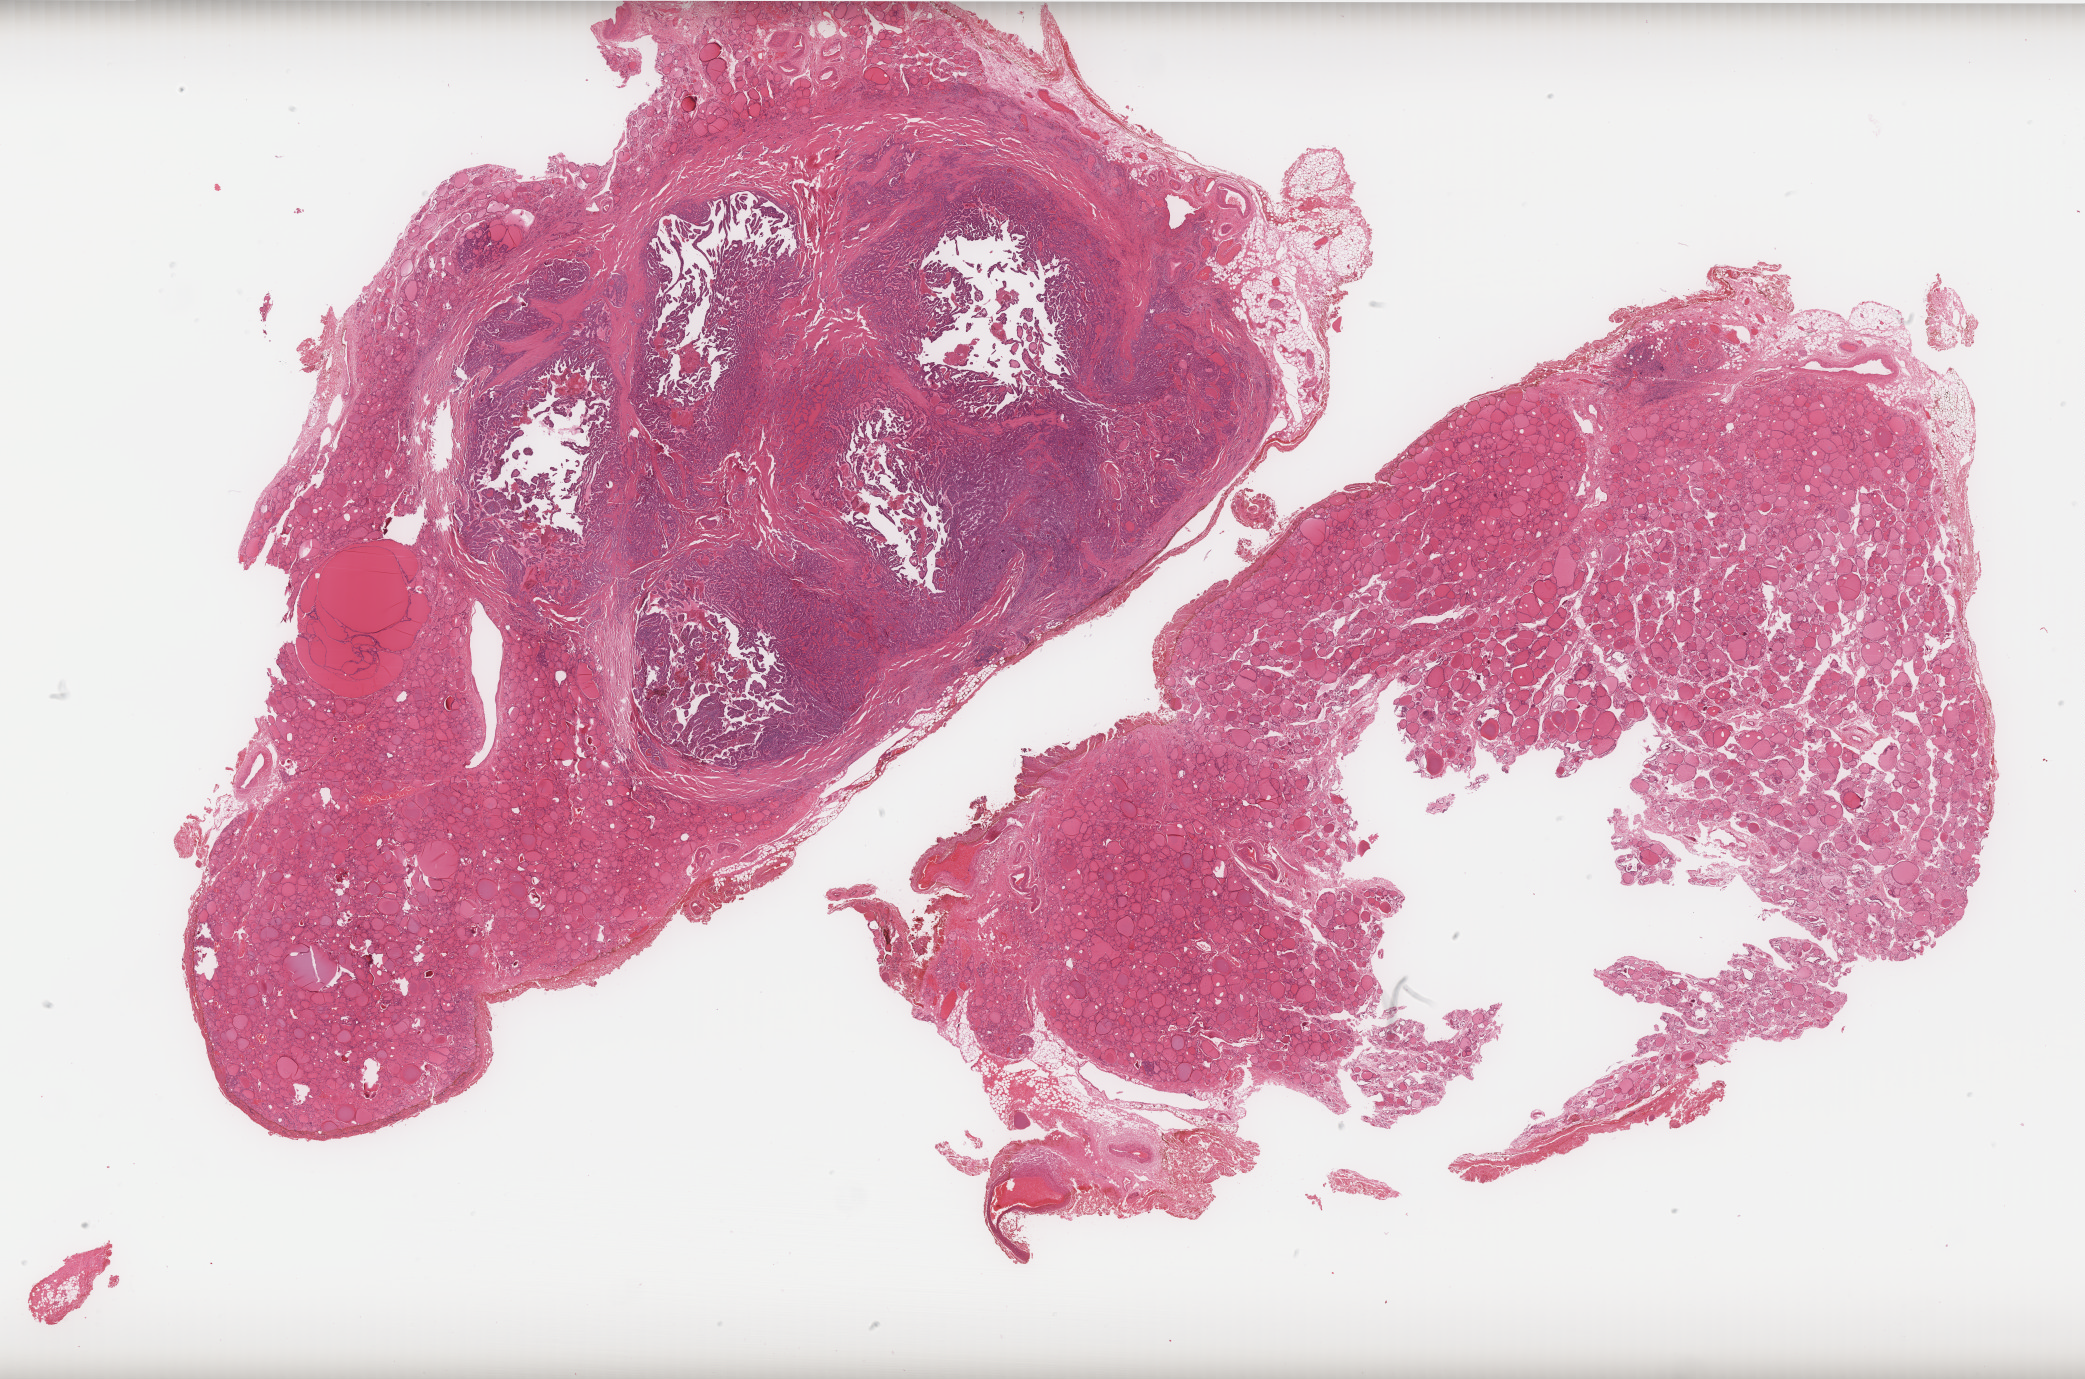
Whole-slide histology image, H&E-stained — a low-resolution overview of the entire scanned area, about 33.4 x 22.1 mm; formalin-fixed paraffin-embedded (FFPE) diagnostic section; primary tumour sample from the thyroid. Male, age 76 years at initial diagnosis.
AJCC pathologic stage: IVA (7th edition). Laterality: right. Lymph nodes positive (case pathology): 1 of 22 examined. Pathologic diagnosis: Papillary adenocarcinoma, NOS.